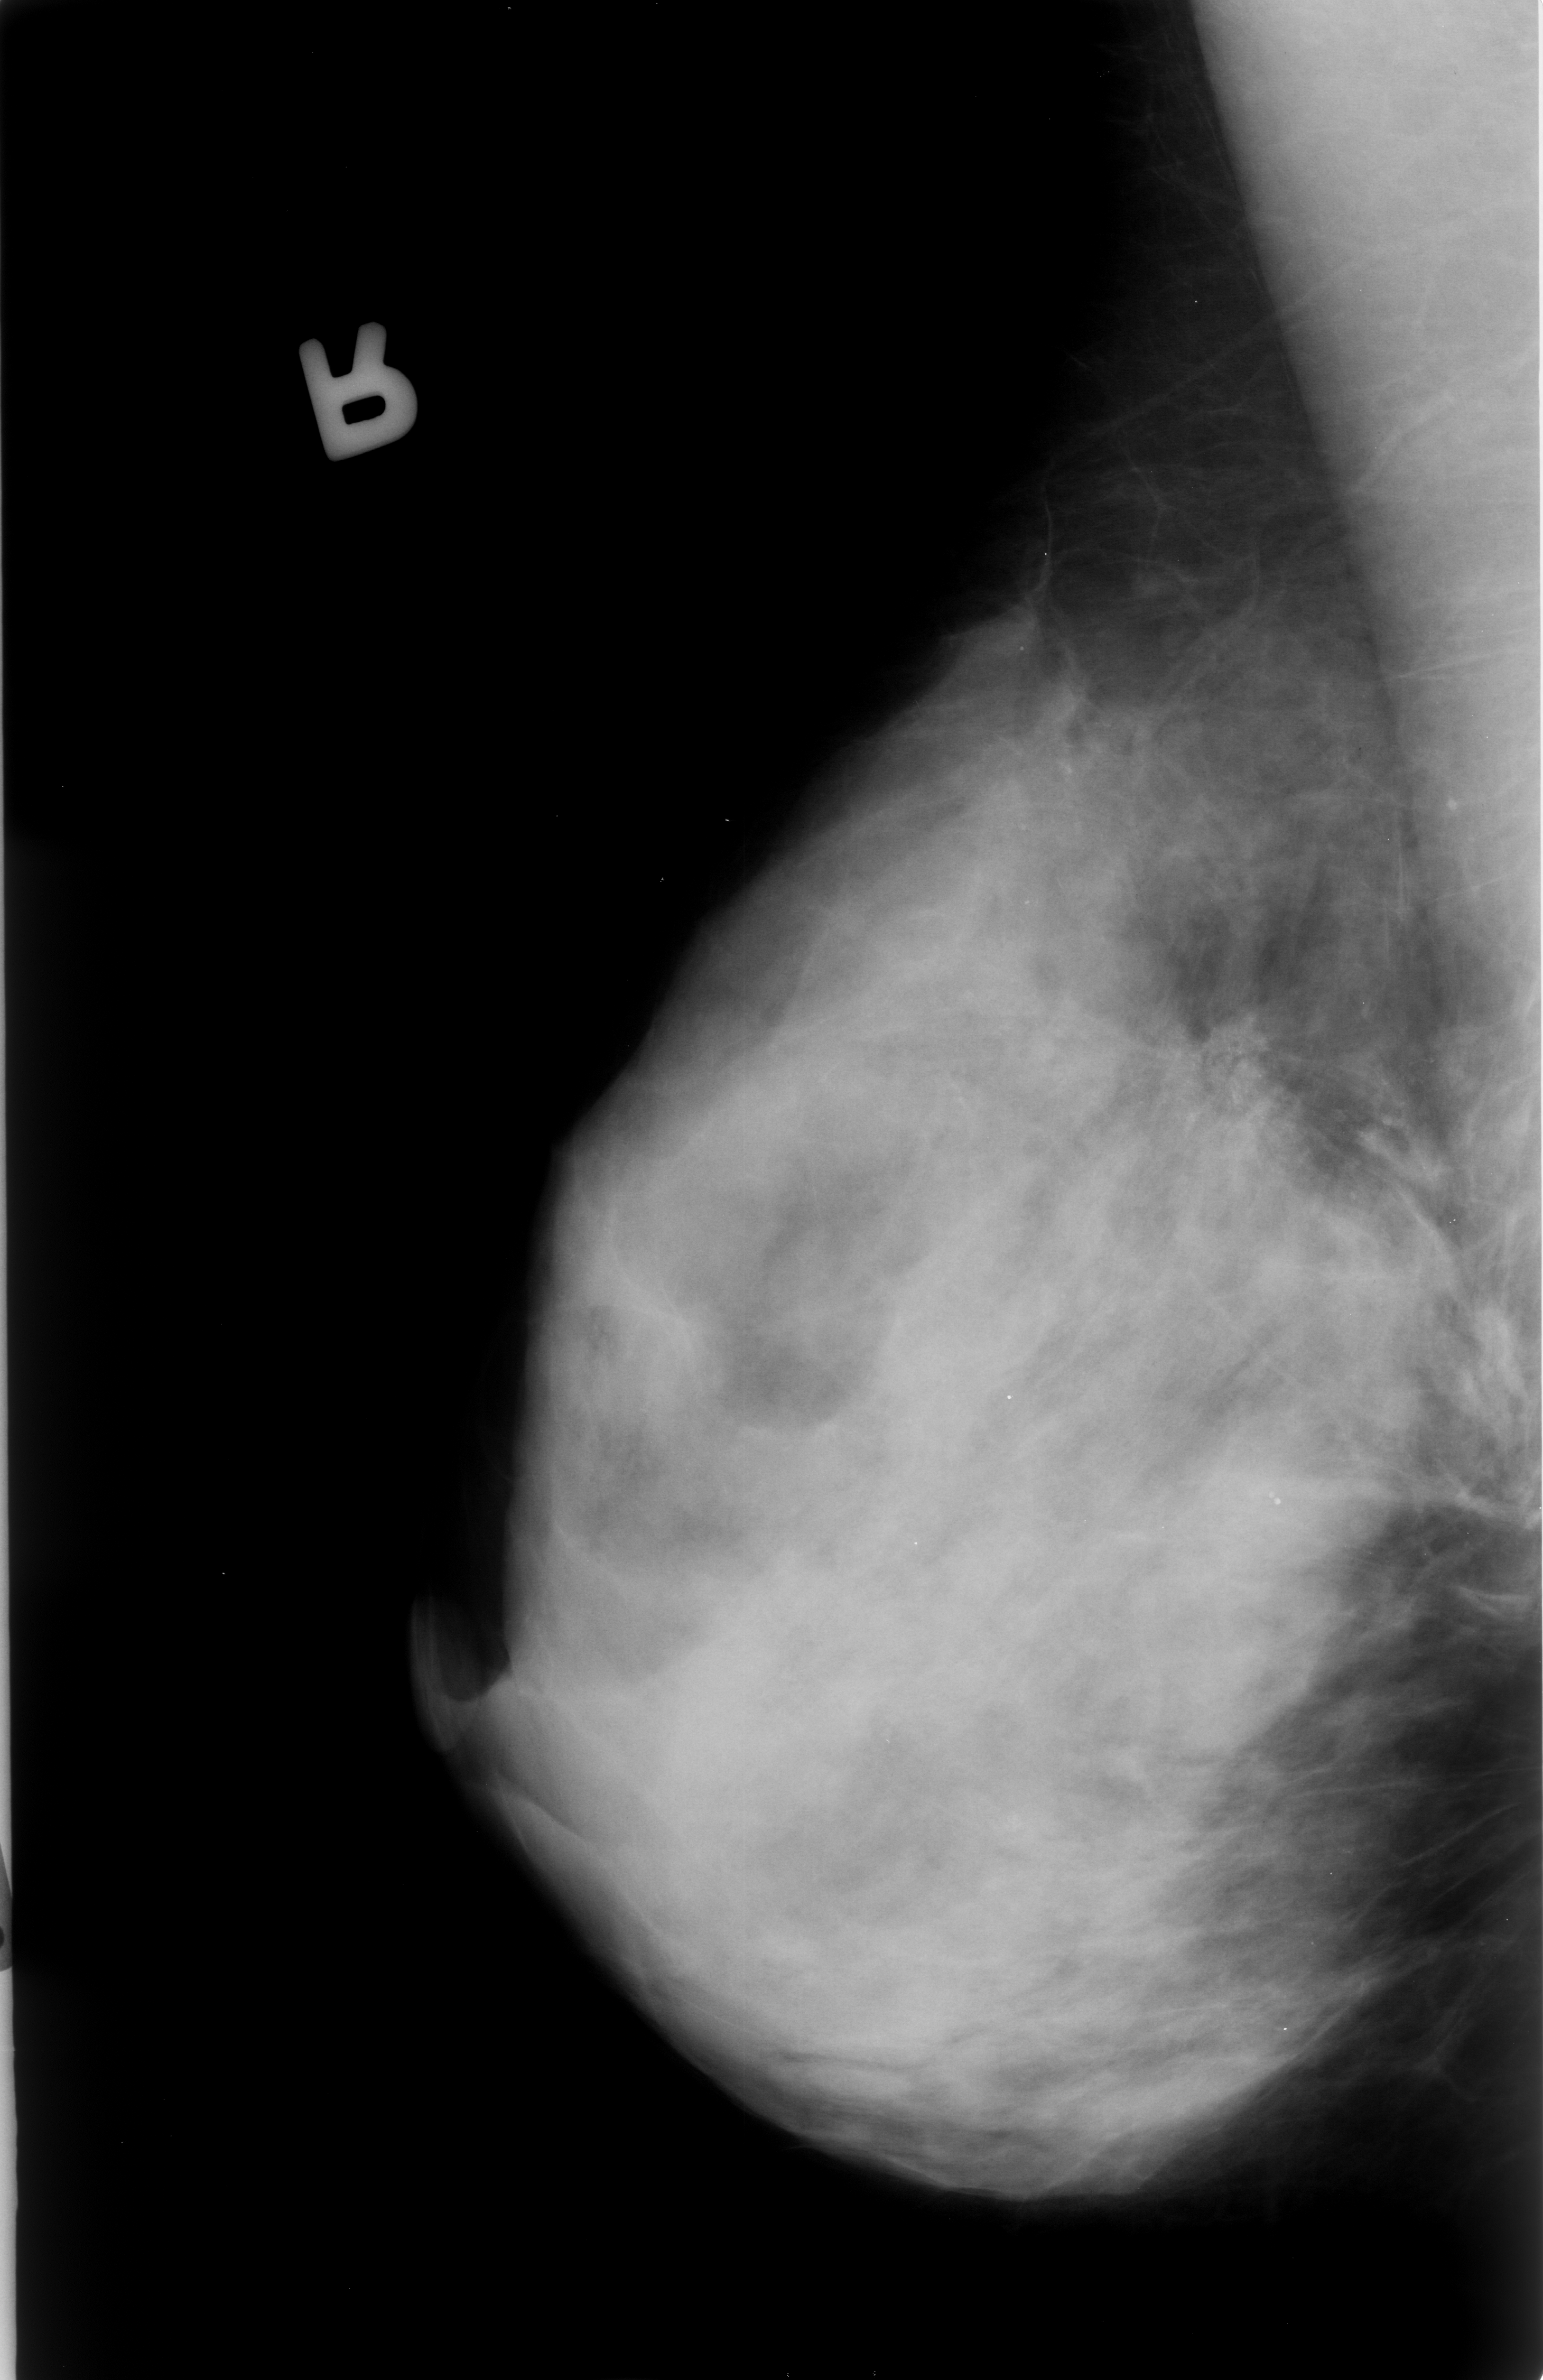
Mammogram (digitized film); right breast; MLO view; breast composition: extremely dense (BI-RADS density category 4 of 4); 1543 × 2380 image matrix.
Marked abnormalities (boxes around the expert regions of interest):
- calcifications, morphology punctate / pleomorphic, distribution clustered; BI-RADS assessment category 4; pathology result (as recorded, not read from the image): malignant: bounding box (x1, y1, x2, y2) in pixels: (1090, 904, 1396, 1202)